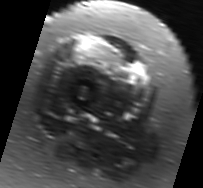
MRI of an extremity soft-tissue mass, one axial slice; T2-weighted fat-saturated; MR volume resampled by the dataset authors to the PET/CT grid (not the native acquisition matrix); 203 × 188 image matrix, field of view 198 × 184 mm. Female patient. From the clinical record (not read from this slice): histological type: malignant solitary fibrous tumor; grade: intermediate; site of the primary tumour: right thigh.
Annotated regions visible in this slice (expert contour drawn on MRI and transferred to this co-registered scan by the dataset authors):
- gross tumour volume including surrounding oedema: box from (x=72, y=35) to (x=148, y=84) px